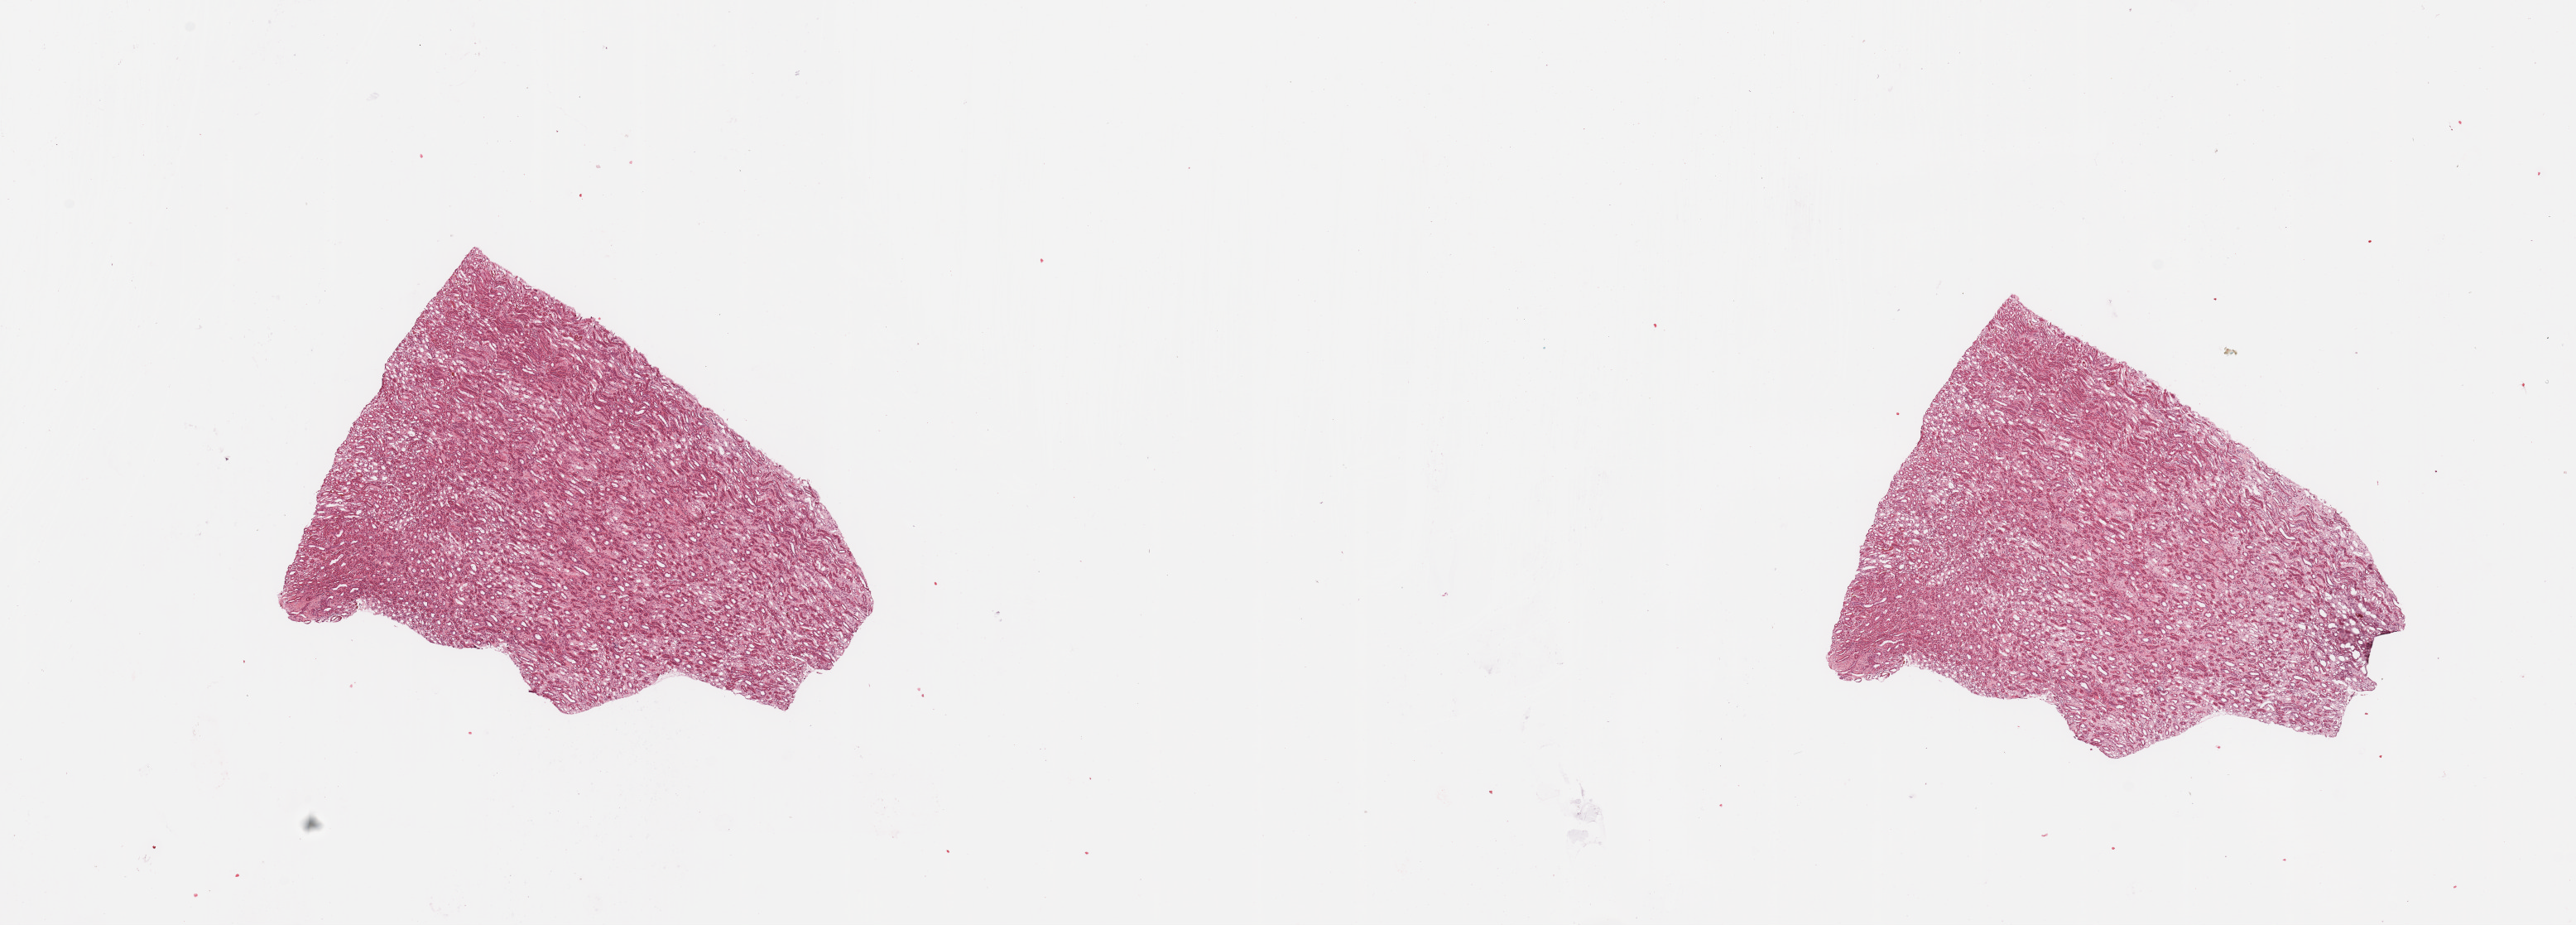
Digitized H&E tissue section (whole slide) — whole scanned area (about 24.6 x 8.8 mm, acquisition: 20x scan) shown as a low-resolution overview. Normal (non-tumour) tissue sample, sampled site: kidney. 58-year-old female patient.
This section: normal (non-tumour) tissue from the same patient. Patient diagnosis: Renal cell carcinoma, NOS.